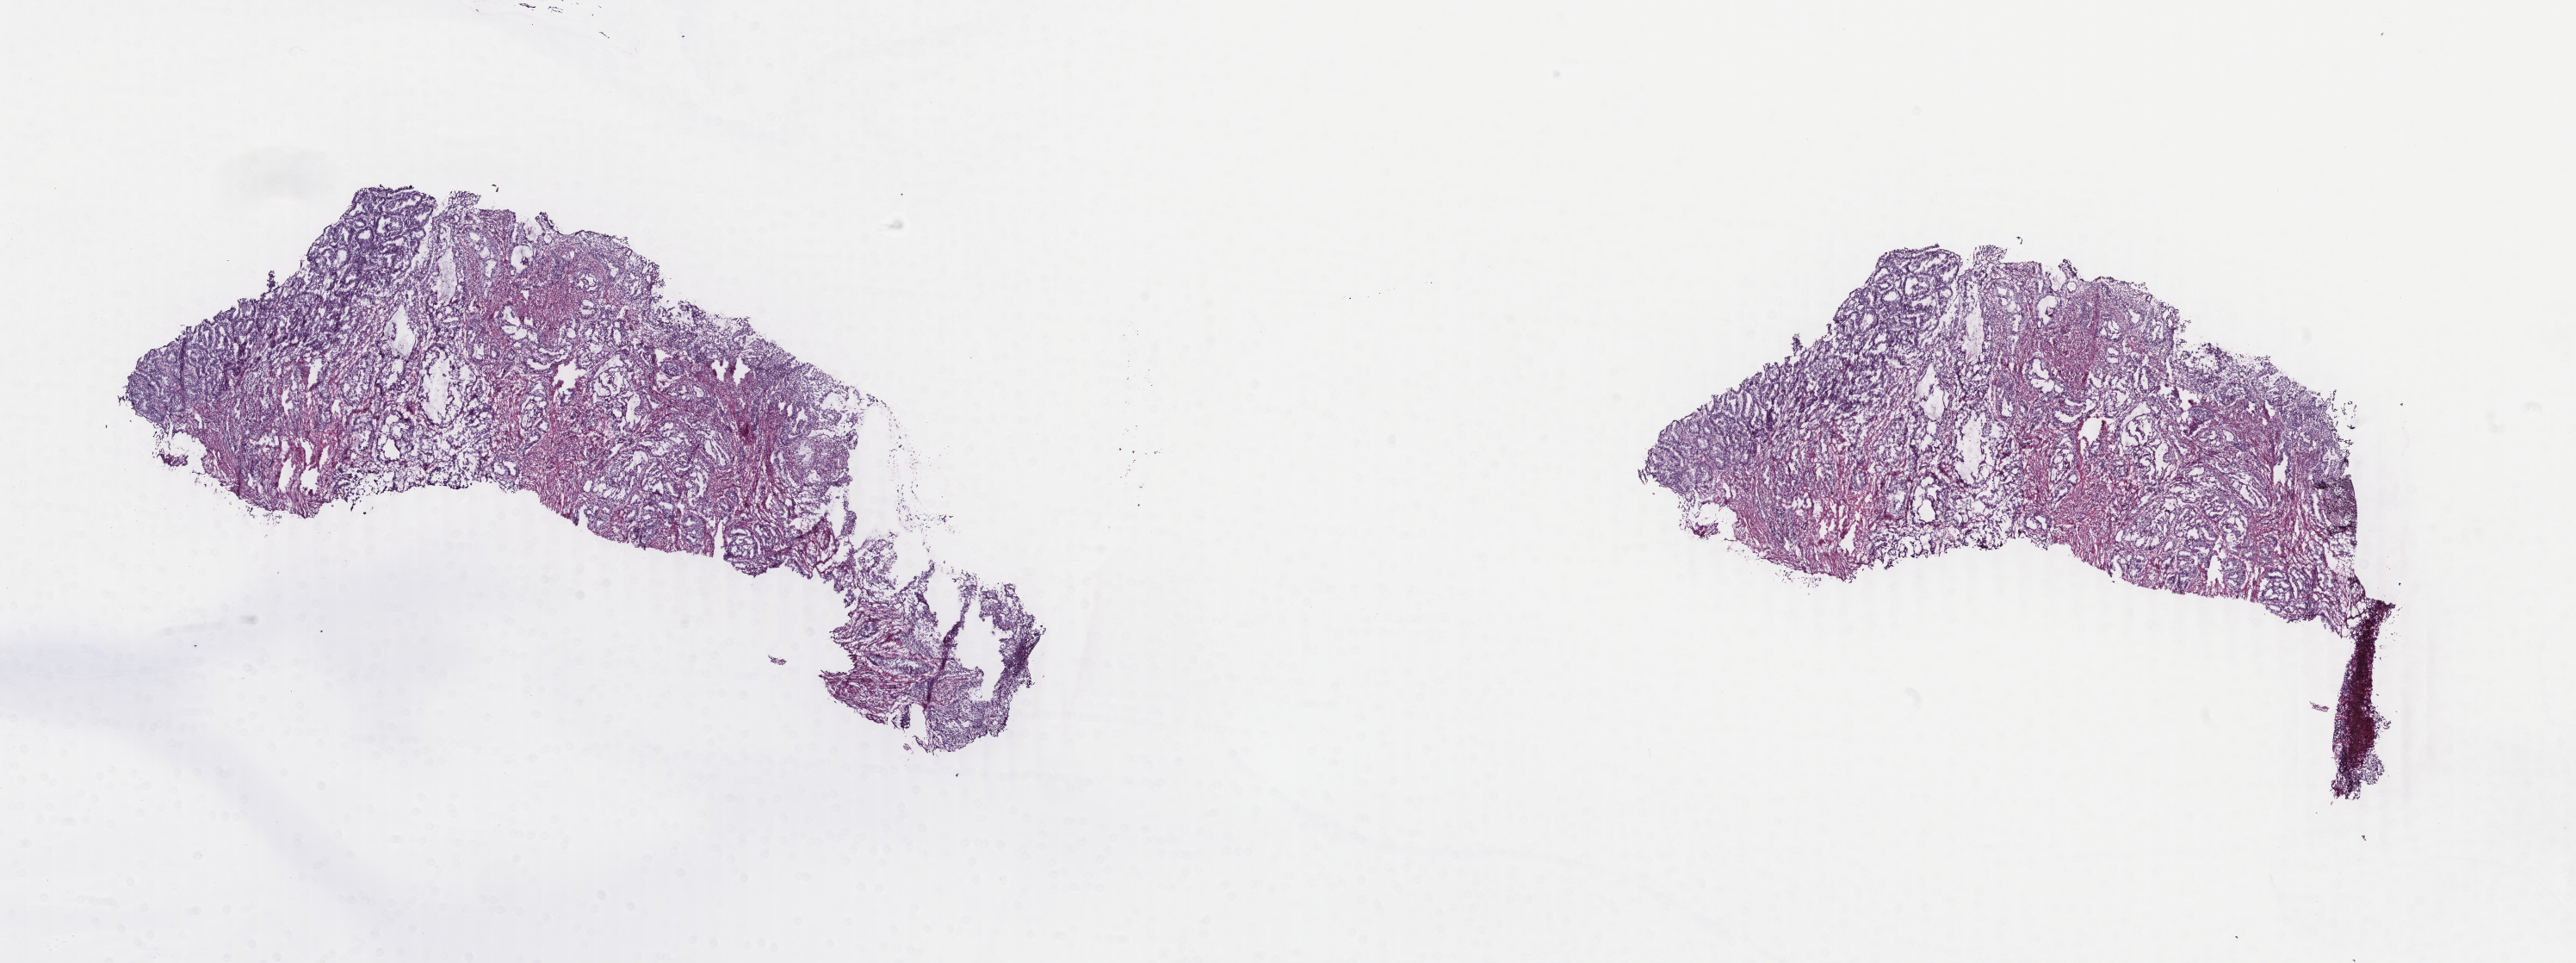
H&E whole-slide image — low-resolution overview of the scanned area, about 23.8 x 8.9 mm (slide scanned at 40x), frozen section from the top of the tissue portion, sample: primary tumour, uterus. Patient: female, age at initial diagnosis 74 years. Histologic grade: G1 (well differentiated). Slide review estimates, as recorded: tumour cells 70%, tumour nuclei 60%, normal cells 0%, stromal cells 30%, necrosis 0%. Inflammatory infiltration, as recorded: lymphocyte infiltration 0%, monocyte infiltration 0%, neutrophil infiltration 0%.
• FIGO stage: IA
• pathologic diagnosis: Endometrioid adenocarcinoma, NOS (endometrium)